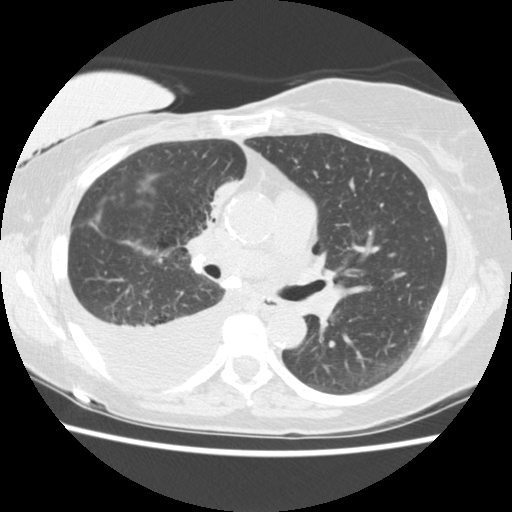
Axial slice from a low-dose chest CT screening exam. Third annual screen. Lung window (W 1500 / L -600 HU). 2.5 mm slice thickness. 512 × 512 image matrix. Female participant, aged 56 years at enrolment. Current smoker at enrolment.
Expert-annotated lung lesion, box from (x=185, y=169) to (x=250, y=236) px. The screening reader recorded 2 non-calcified nodules or masses ≥4 mm on this exam (right middle lobe, right lower lobe); which of them this box marks is not recorded.